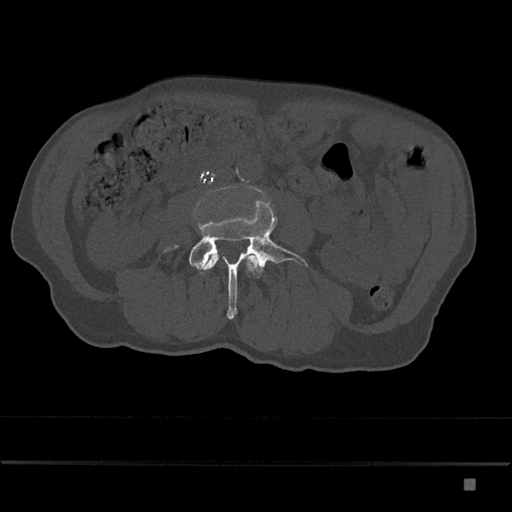
CT including the spine, one axial slice; slice 357 of 797 in the series (ordered by position); reconstruction kernel Br40s/3; 120 kVp; bone window (W 1800 / L 400 HU); 0.5 mm slice thickness; 512 × 512 image matrix, field of view 390 × 390 mm. Patient: male, 72 years. Case-level facts recorded for this patient, not image findings: primary cancer: prostate.
Annotated regions visible in this slice (semi-automatic segmentation, software-assisted and operator-edited):
- L3 vertebra: bounding box [x1, y1, x2, y2] px = [203, 254, 259, 271]
- L4 vertebra: [163, 200, 309, 319]